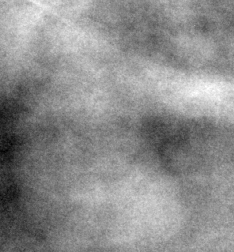
Crop from a digitized film mammogram around one marked abnormality; right breast; CC view; BI-RADS breast density category 2 (scale 1–4).
- Finding: mass, shape lobulated, margins circumscribed; BI-RADS assessment category 3; pathology (as recorded): benign.